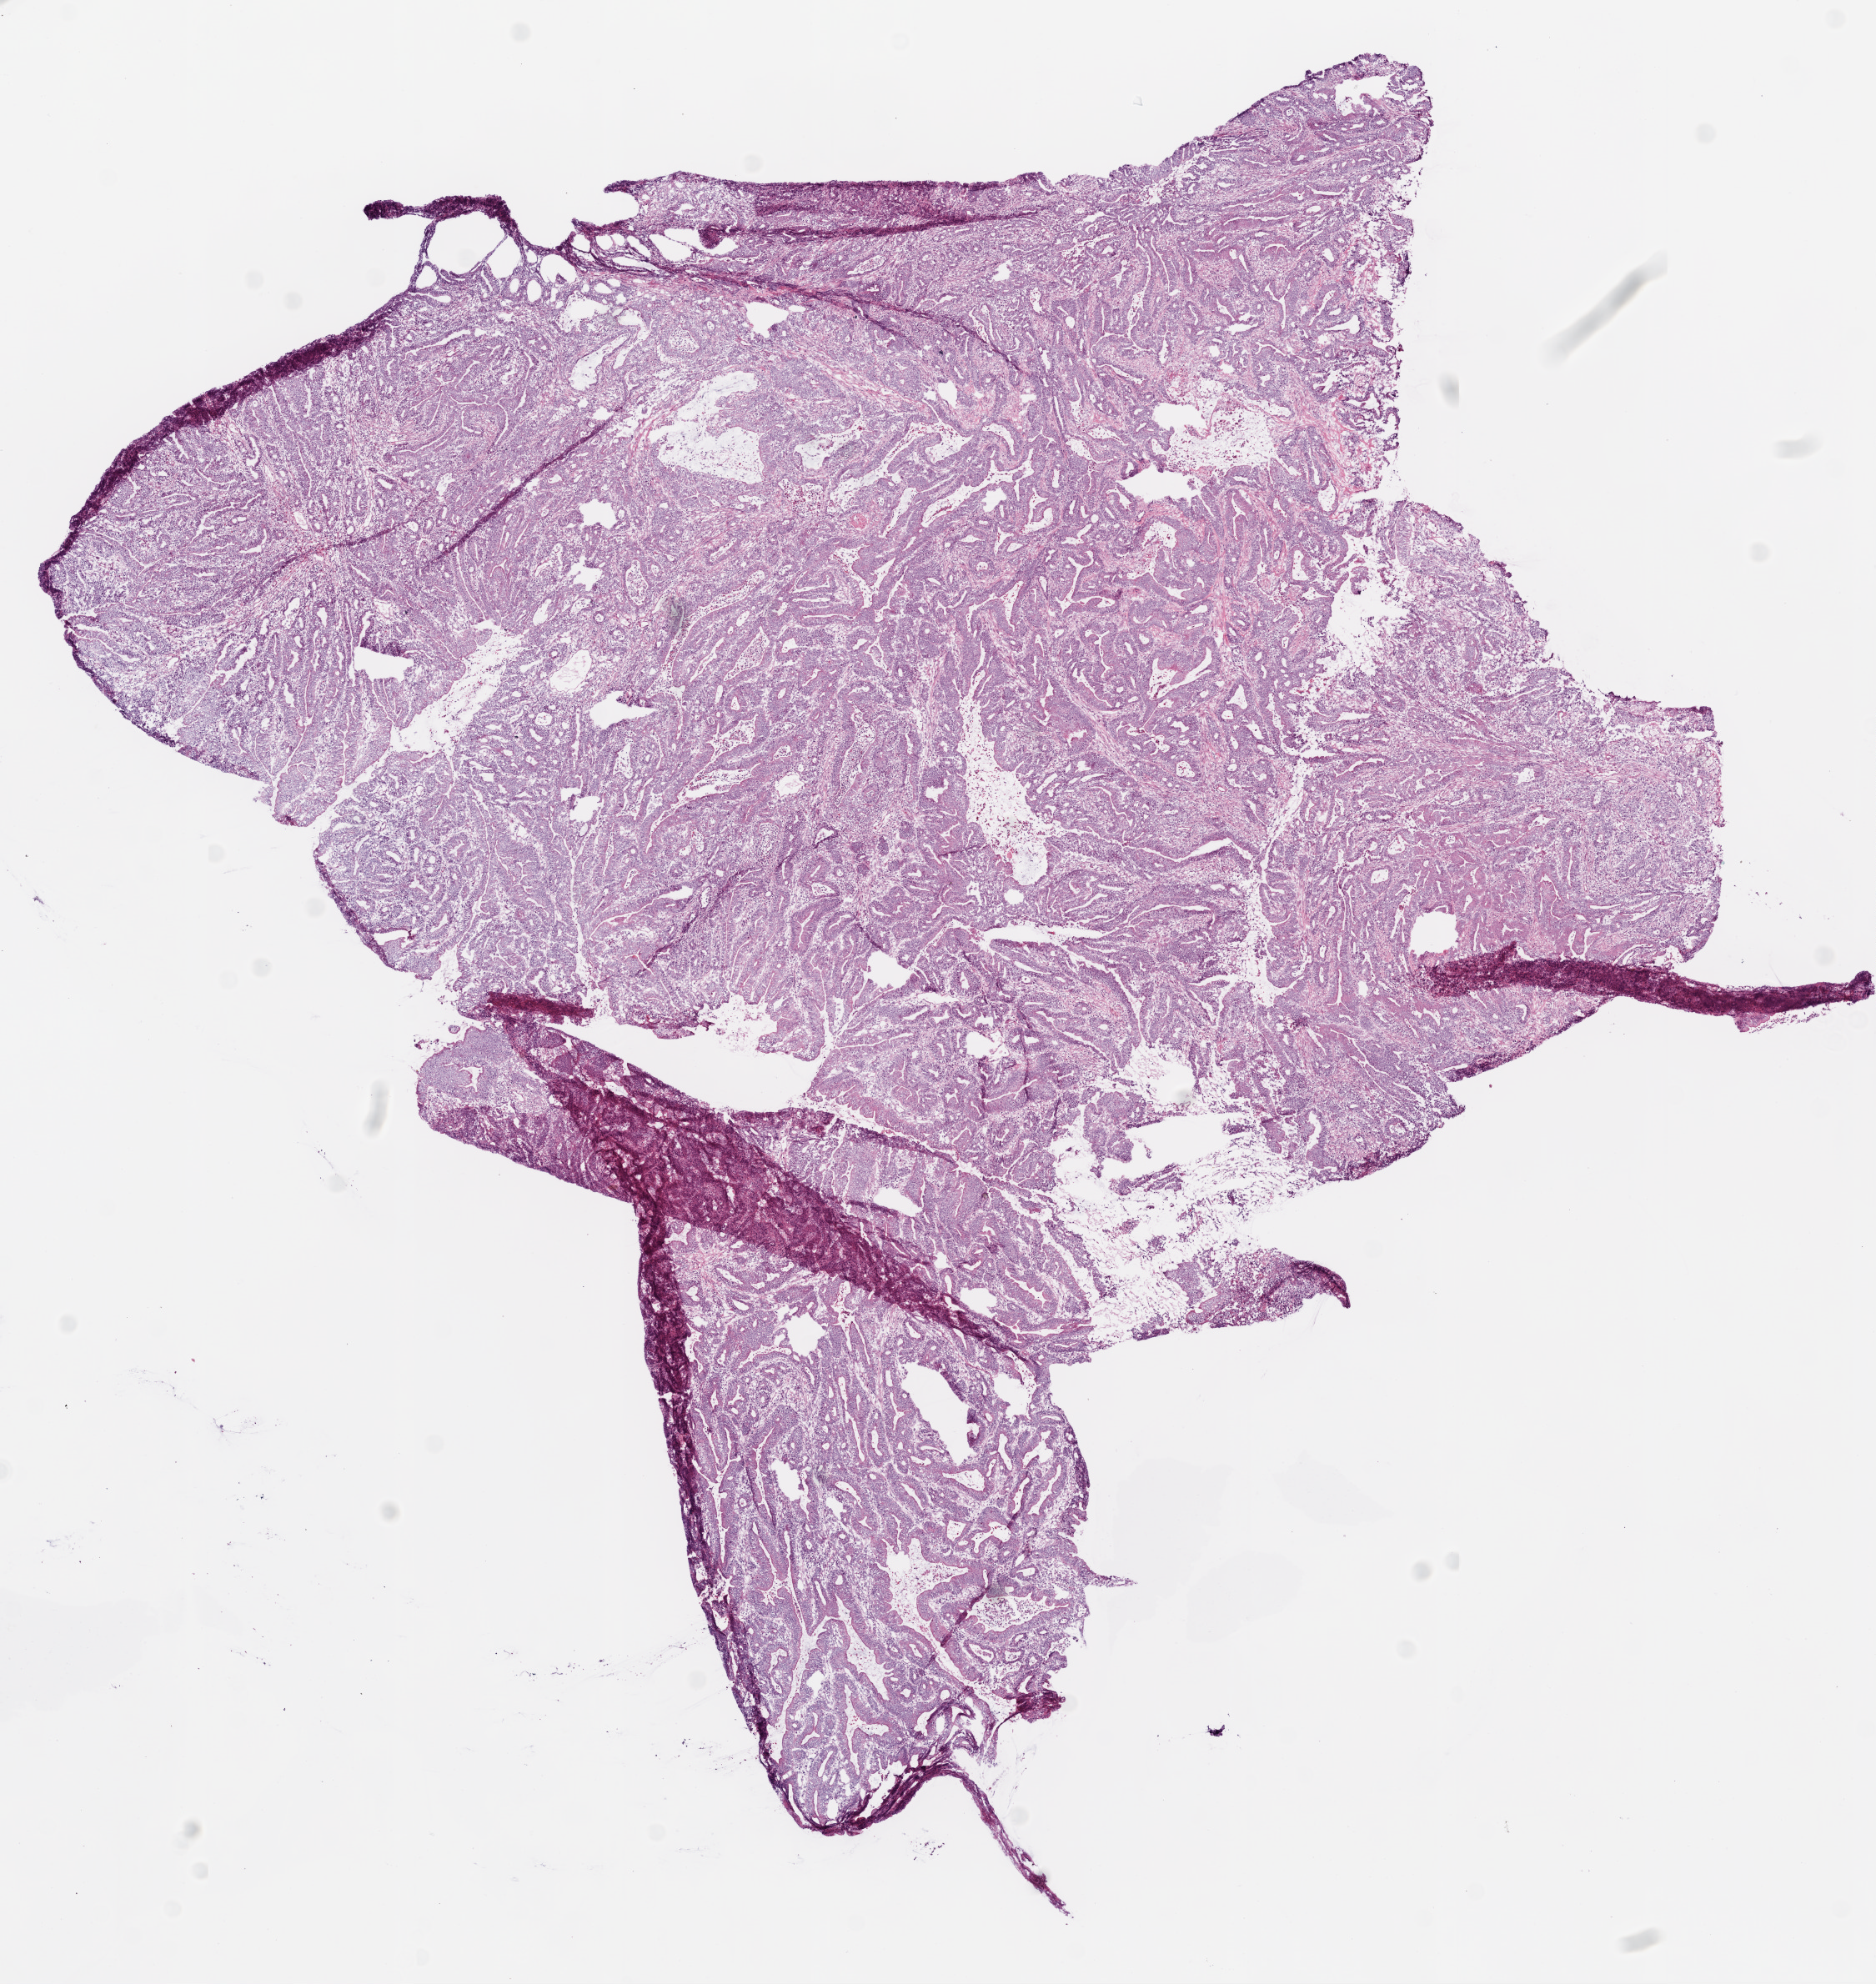
Whole-slide histology image, H&E-stained, low-resolution overview of the scanned area, about 9.0 x 9.5 mm; frozen section; colon, primary tumour sample. Patient: male, age at initial diagnosis 84 years. Slide review estimates, as recorded: tumour cells 60%, tumour nuclei 70%, normal cells 0%, stromal cells 38%, necrosis 2%.
* lymph nodes positive (case pathology): 0 of 25 examined
* AJCC pathologic stage: I (6th edition)
* pathologic diagnosis: Mucinous adenocarcinoma (ascending colon)